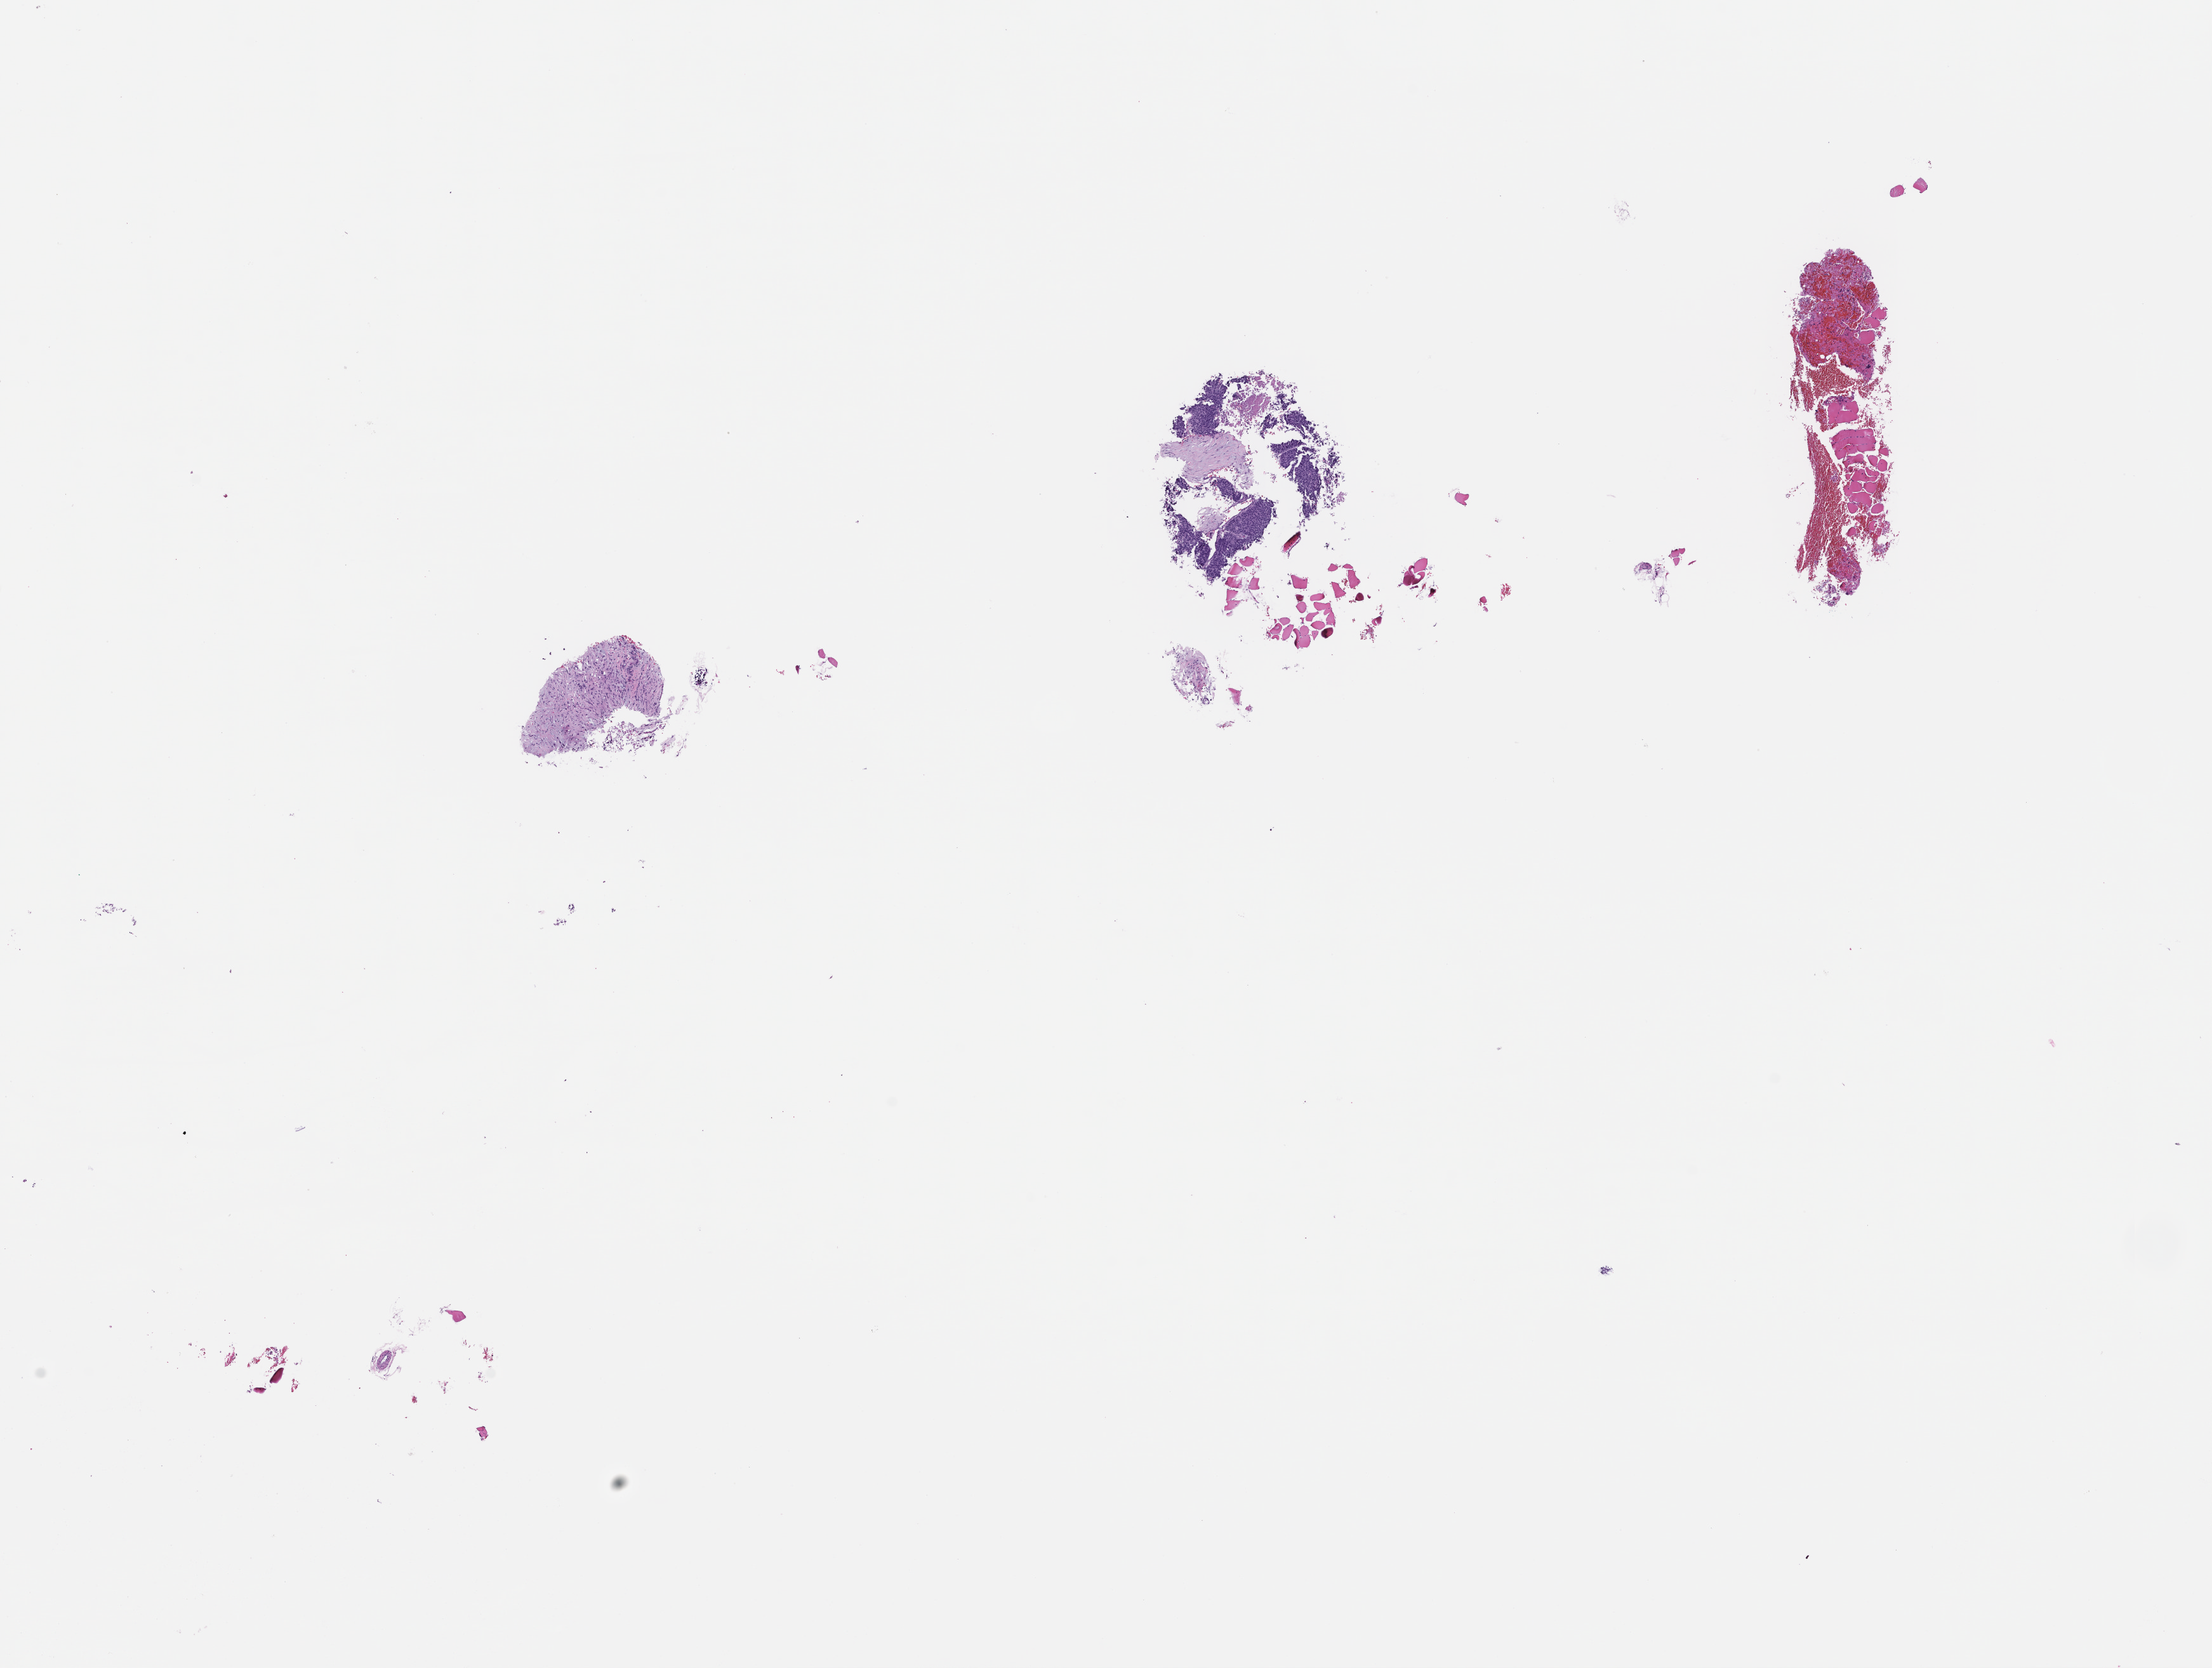
Whole-slide image, H&E stain, low-resolution overview of the scanned area, about 14.1 x 10.6 mm; FFPE section. Patient: male.
• this section: metastatic tumor tissue
• patient diagnosis (primary): Prostate Carcinoma